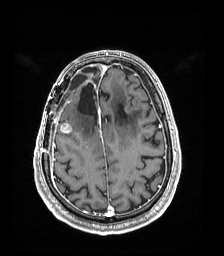
Brain MRI from a brain-tumour surgery series, one axial slice; T1-weighted post-contrast; 1 mm slice thickness; 224 × 256 image matrix, field of view 224 × 256 mm. Case-level facts recorded for this patient, not image findings: histopathology: Astrocytoma; WHO grade: 4; IDH mutation: yes; tumour location: Right Frontal.
Annotated regions visible in this slice (outlined manually by an expert reader):
- previous resection cavity: bounding box (x1, y1, x2, y2) in pixels: (78, 83, 98, 122)